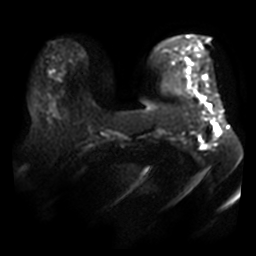
Breast MRI, one axial slice. Position 10 of 40 along the scan axis. Diffusion-weighted series; image 2 of 4 stored at this slice position (different b-values; order by instance number). 3 T. 5 mm slice thickness. 256 × 256 image matrix, field of view 400 × 400 mm. Female patient.
Annotated regions visible in this slice (outlined manually by an expert reader):
- tumour on diffusion-weighted imaging: box from (x=216, y=127) to (x=221, y=134) px